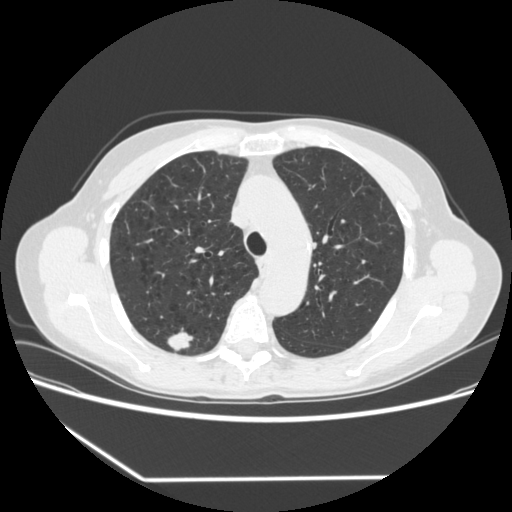
Low-dose screening chest CT, one axial slice; position 244 of 323 along the scan axis; reconstruction kernel STANDARD; lung window (W 1500 / L -600 HU); 1.25 mm slice thickness; 512 × 512 image matrix, field of view 360 × 360 mm.
Structures marked on this image (expert manual segmentation):
- lesion 1 (tumor, upper lobe of right lung): bounding box <167,328,193,351> (left, top, right, bottom; pixels)